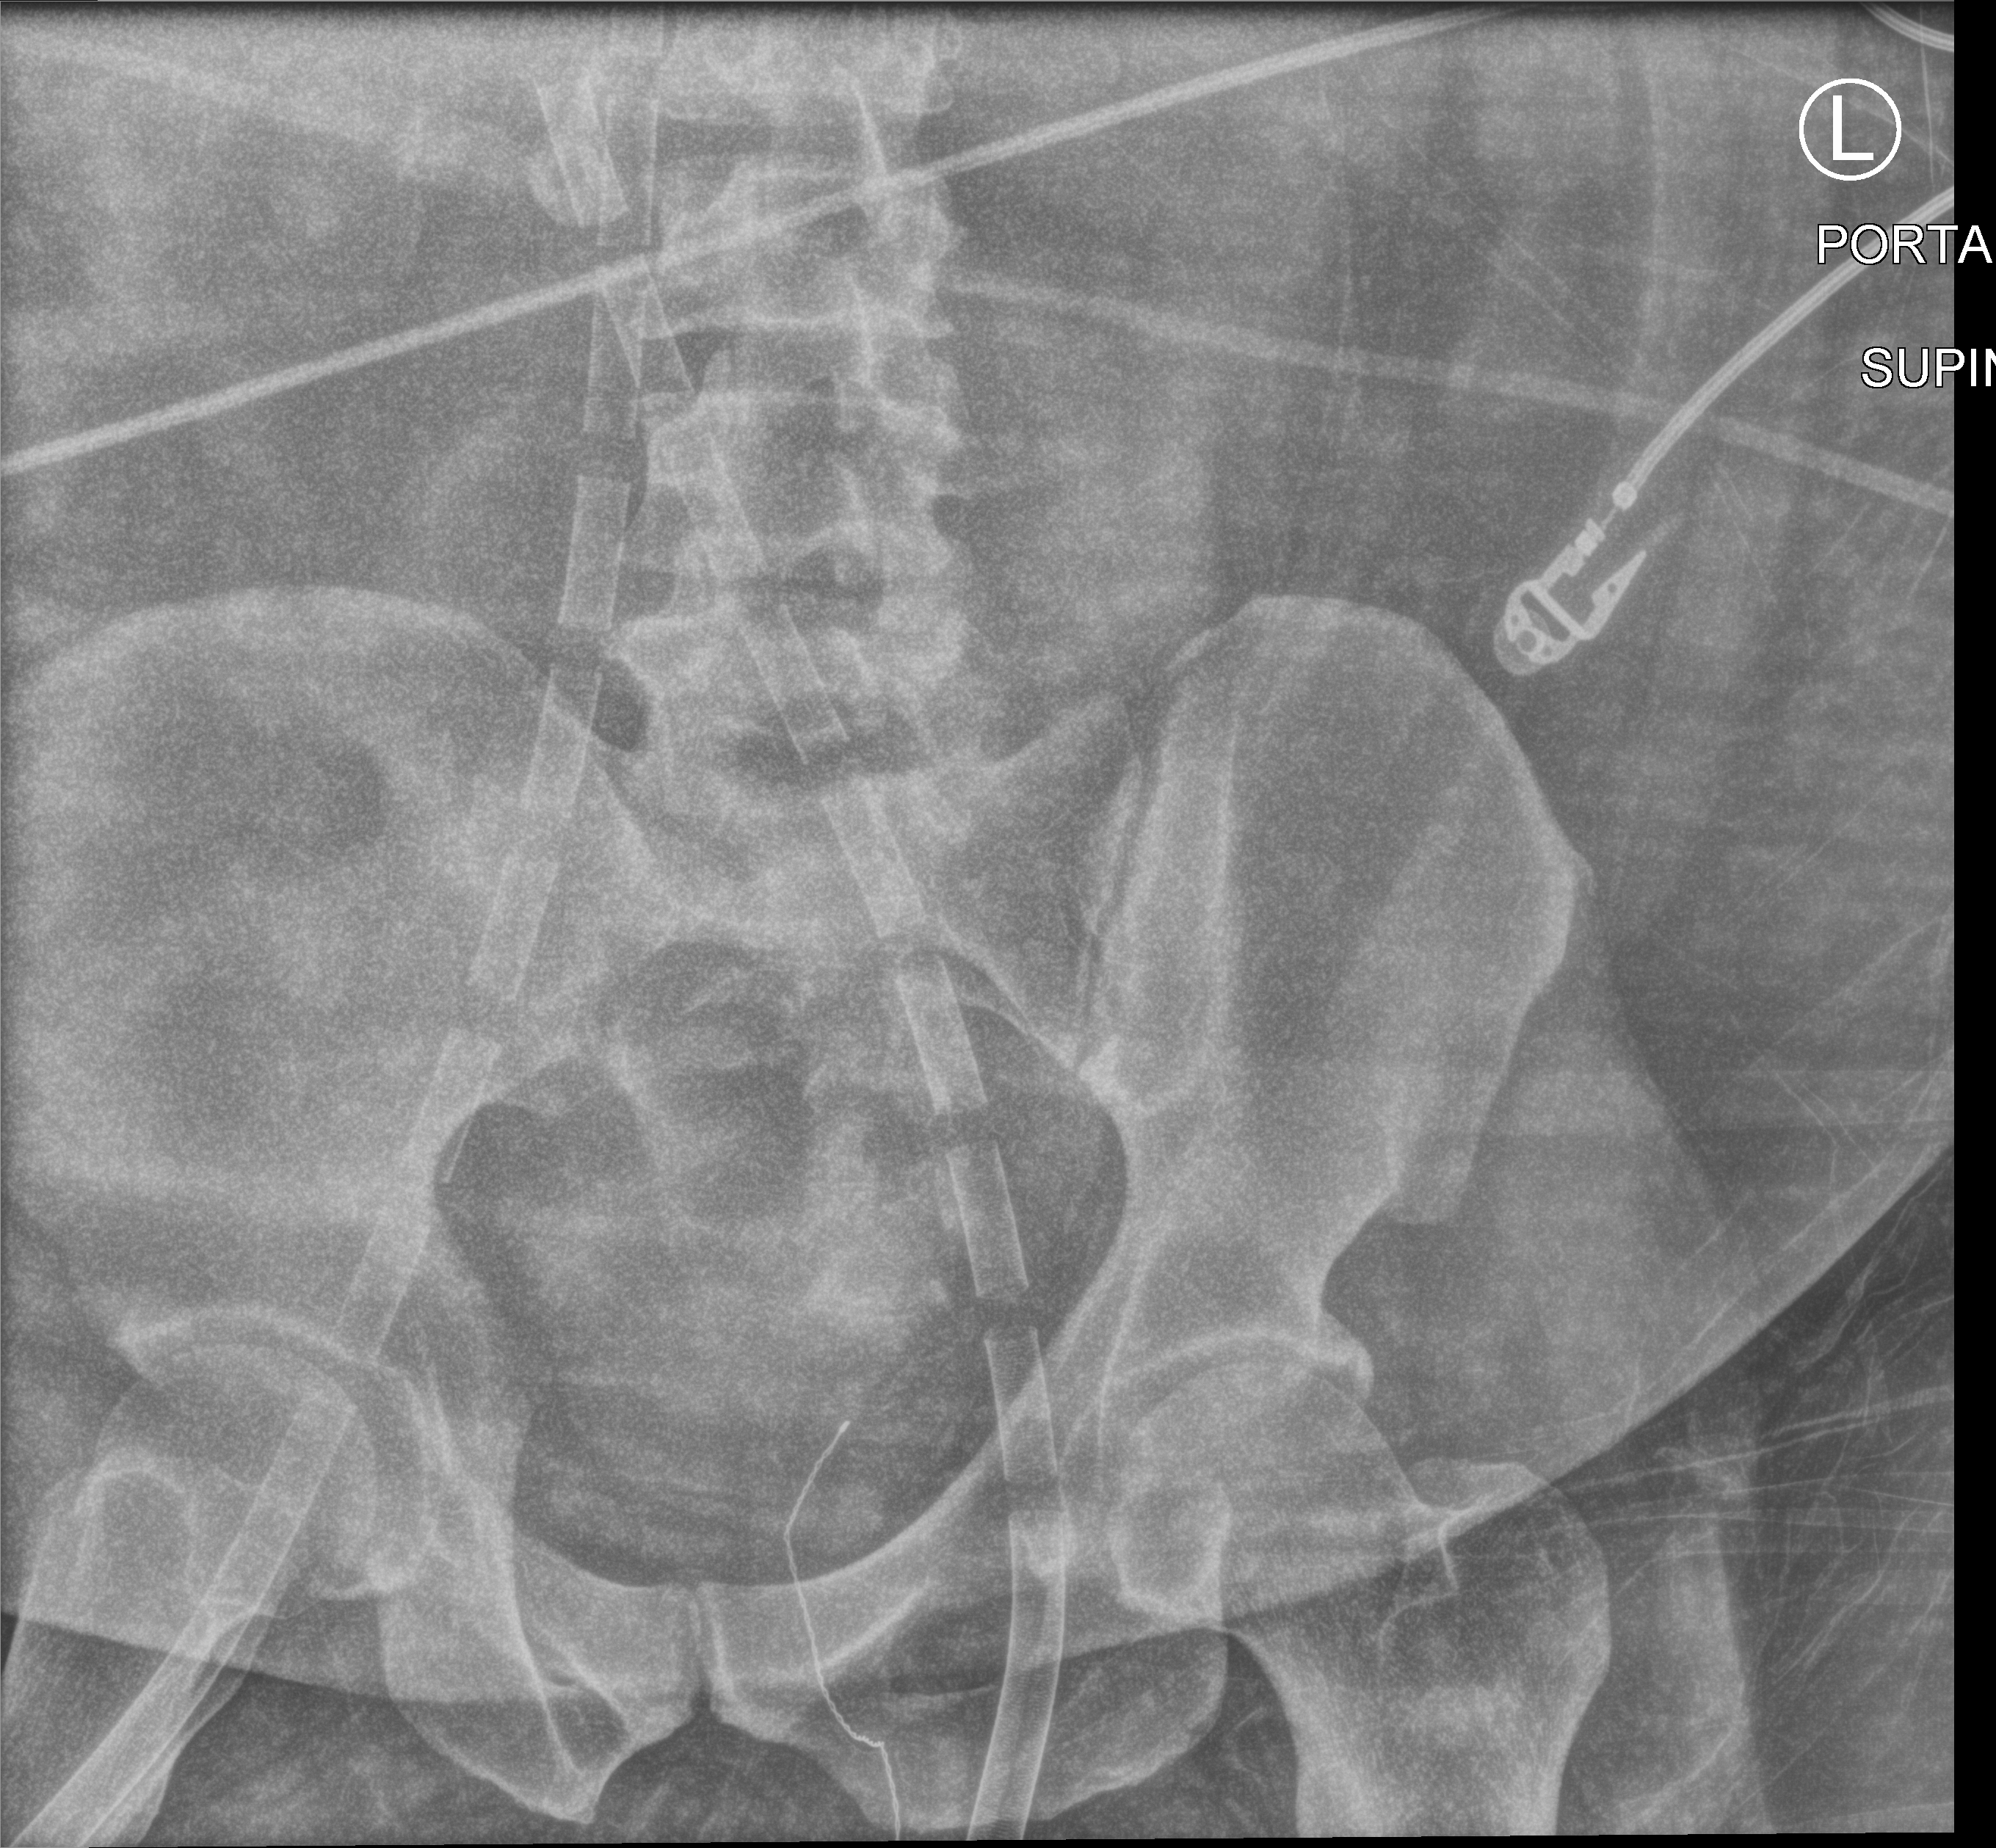
Bedside abdomen radiograph (computed radiography), anteroposterior (AP) projection. Adult patient hospitalised with COVID-19, age 18–59 years.
Hospital-stay facts (about this admission, not read from this image; timing relative to this image not recorded):
- admitted to intensive care during this hospital stay: yes
- chronic kidney disease (admission record): no